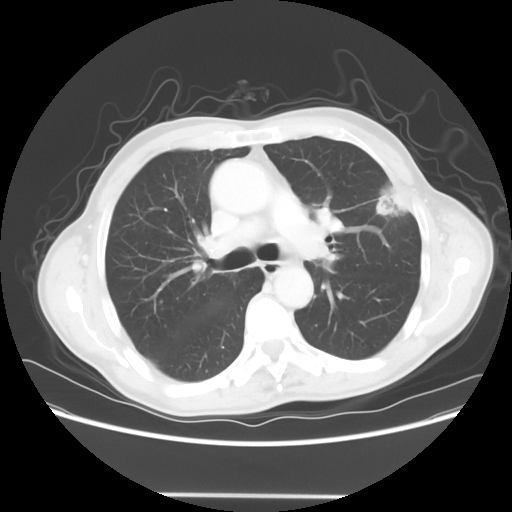
Chest CT, one axial slice. Slice 40 of 64 in the series (ordered by position). Reconstruction kernel STANDARD. Lung window (W 1500 / L -600 HU). 512 × 512 image matrix. Male patient, age 71 years. From the clinical record (not read from this slice): clinical TNM (as recorded): T1c N0 M0; histopathological grade: G2-3.
Structures marked on this image (bounding box drawn by a radiologist):
- lung tumour (recorded histology: adenocarcinoma): box from (x=369, y=180) to (x=411, y=224) px